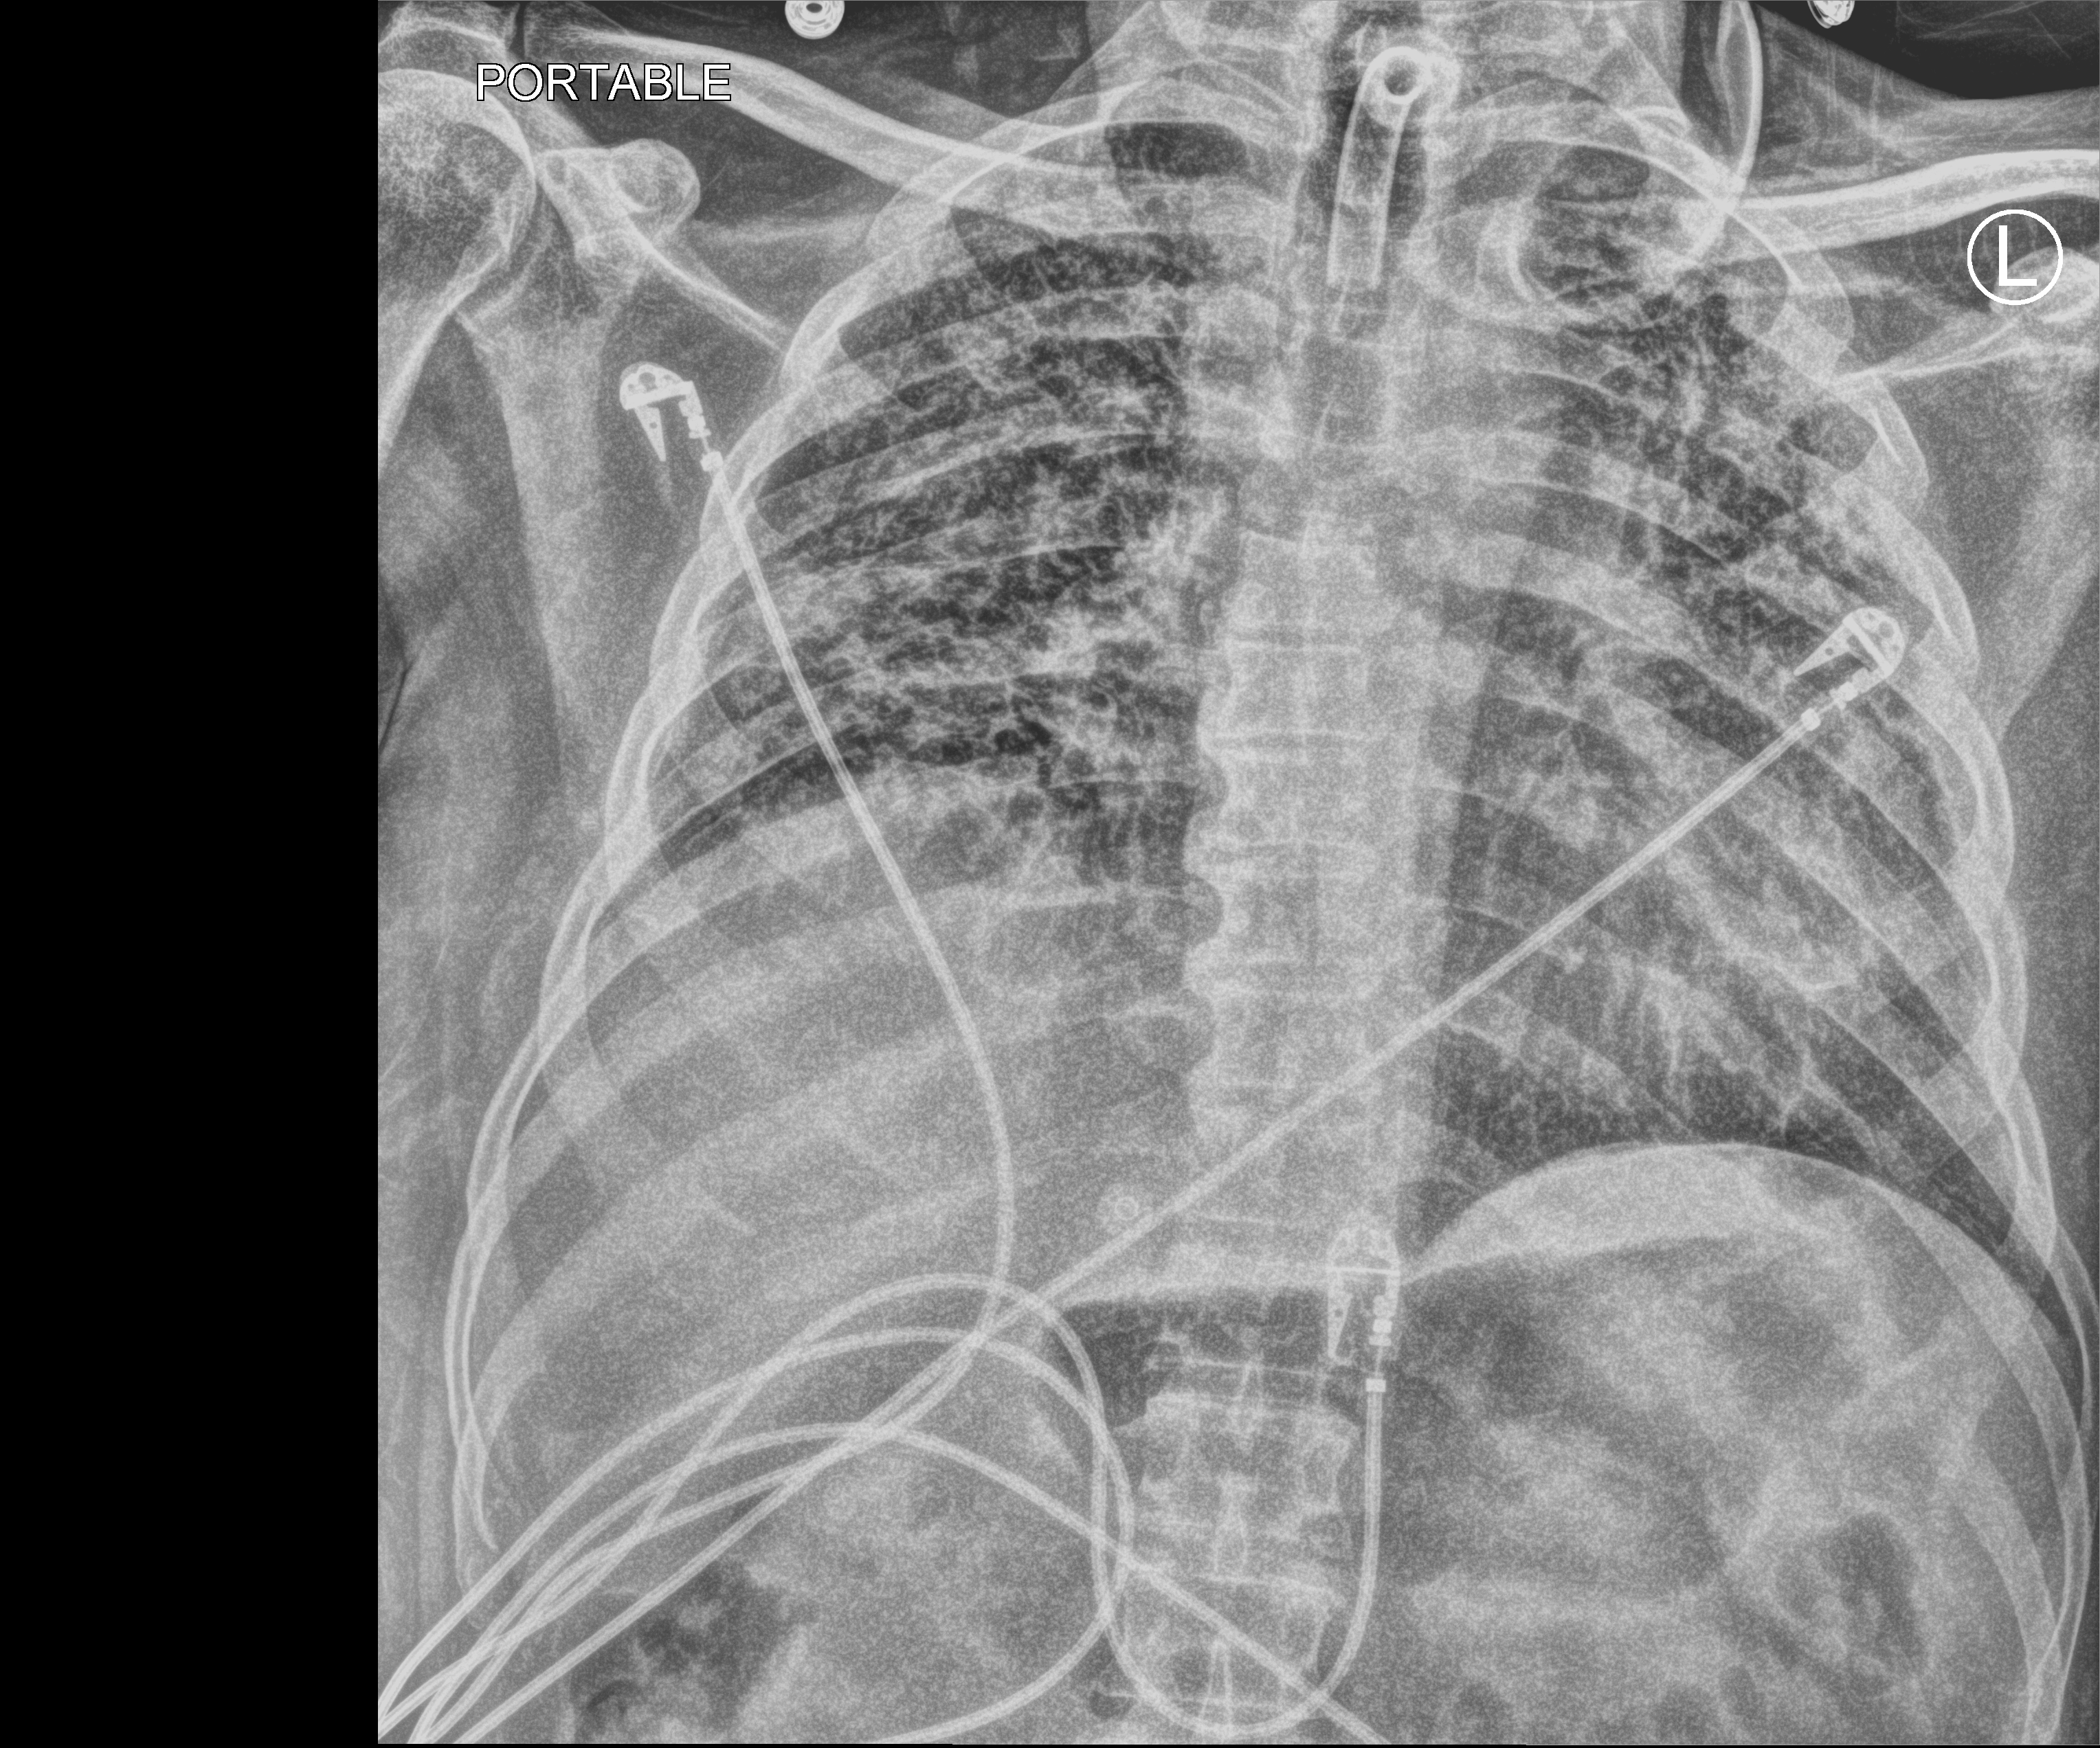
Portable chest radiograph; anteroposterior (AP) projection. Male patient hospitalised with COVID-19, age 18–59 years.
Hospital-stay facts (about this admission, not read from this image; timing relative to this image not recorded):
- length of hospital stay: 83 days
- admitted to intensive care during this hospital stay: yes
- diabetes (admission record): no